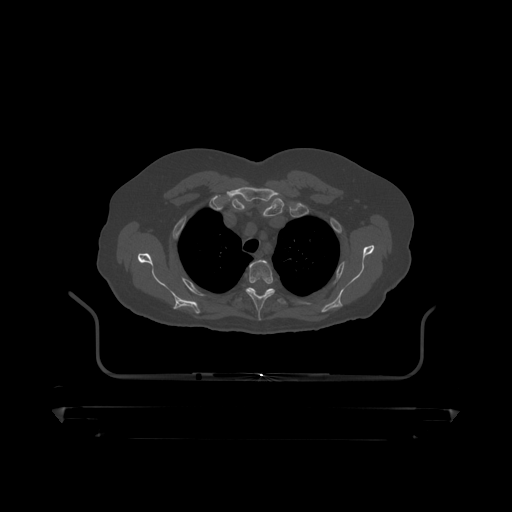
CT including the spine, one axial slice; slice 354 of 390 in the series (ordered by position); bone window (W 1800 / L 400 HU); 1.25 mm slice thickness; 512 × 512 image matrix, field of view 650 × 650 mm. Patient: male, 60 years. From the clinical record (not read from this slice): primary cancer: prostate.
Annotated regions visible in this slice (semi-automatic segmentation, software-assisted and operator-edited):
- T3 vertebra: bounding box [x1, y1, x2, y2] px = [247, 260, 274, 318]
- T4 vertebra: [235, 288, 287, 306]